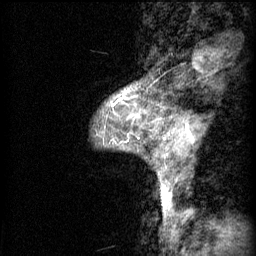
Breast MRI (dynamic contrast-enhanced), one sagittal slice. Slice 15 of 60 in the series (ordered by position). 3 images stored at this slice position (order not interpretable as contrast timing). 1.5 T. TE 4.2 ms, TR 11 ms. 256 × 256 image matrix, field of view 200 × 200 mm. Patient: female, 48 years.
Outlined on this slice (semi-automatic segmentation, software-assisted and operator-edited):
- analysis volume of interest (the breast-tissue region the enhancement analysis was run in; not a lesion): bounding box <113,88,139,107> (left, top, right, bottom; pixels)
- tumour enhancement mask (voxels above the 70 % enhancement threshold inside the analysis volume of interest): <113,100,120,107>